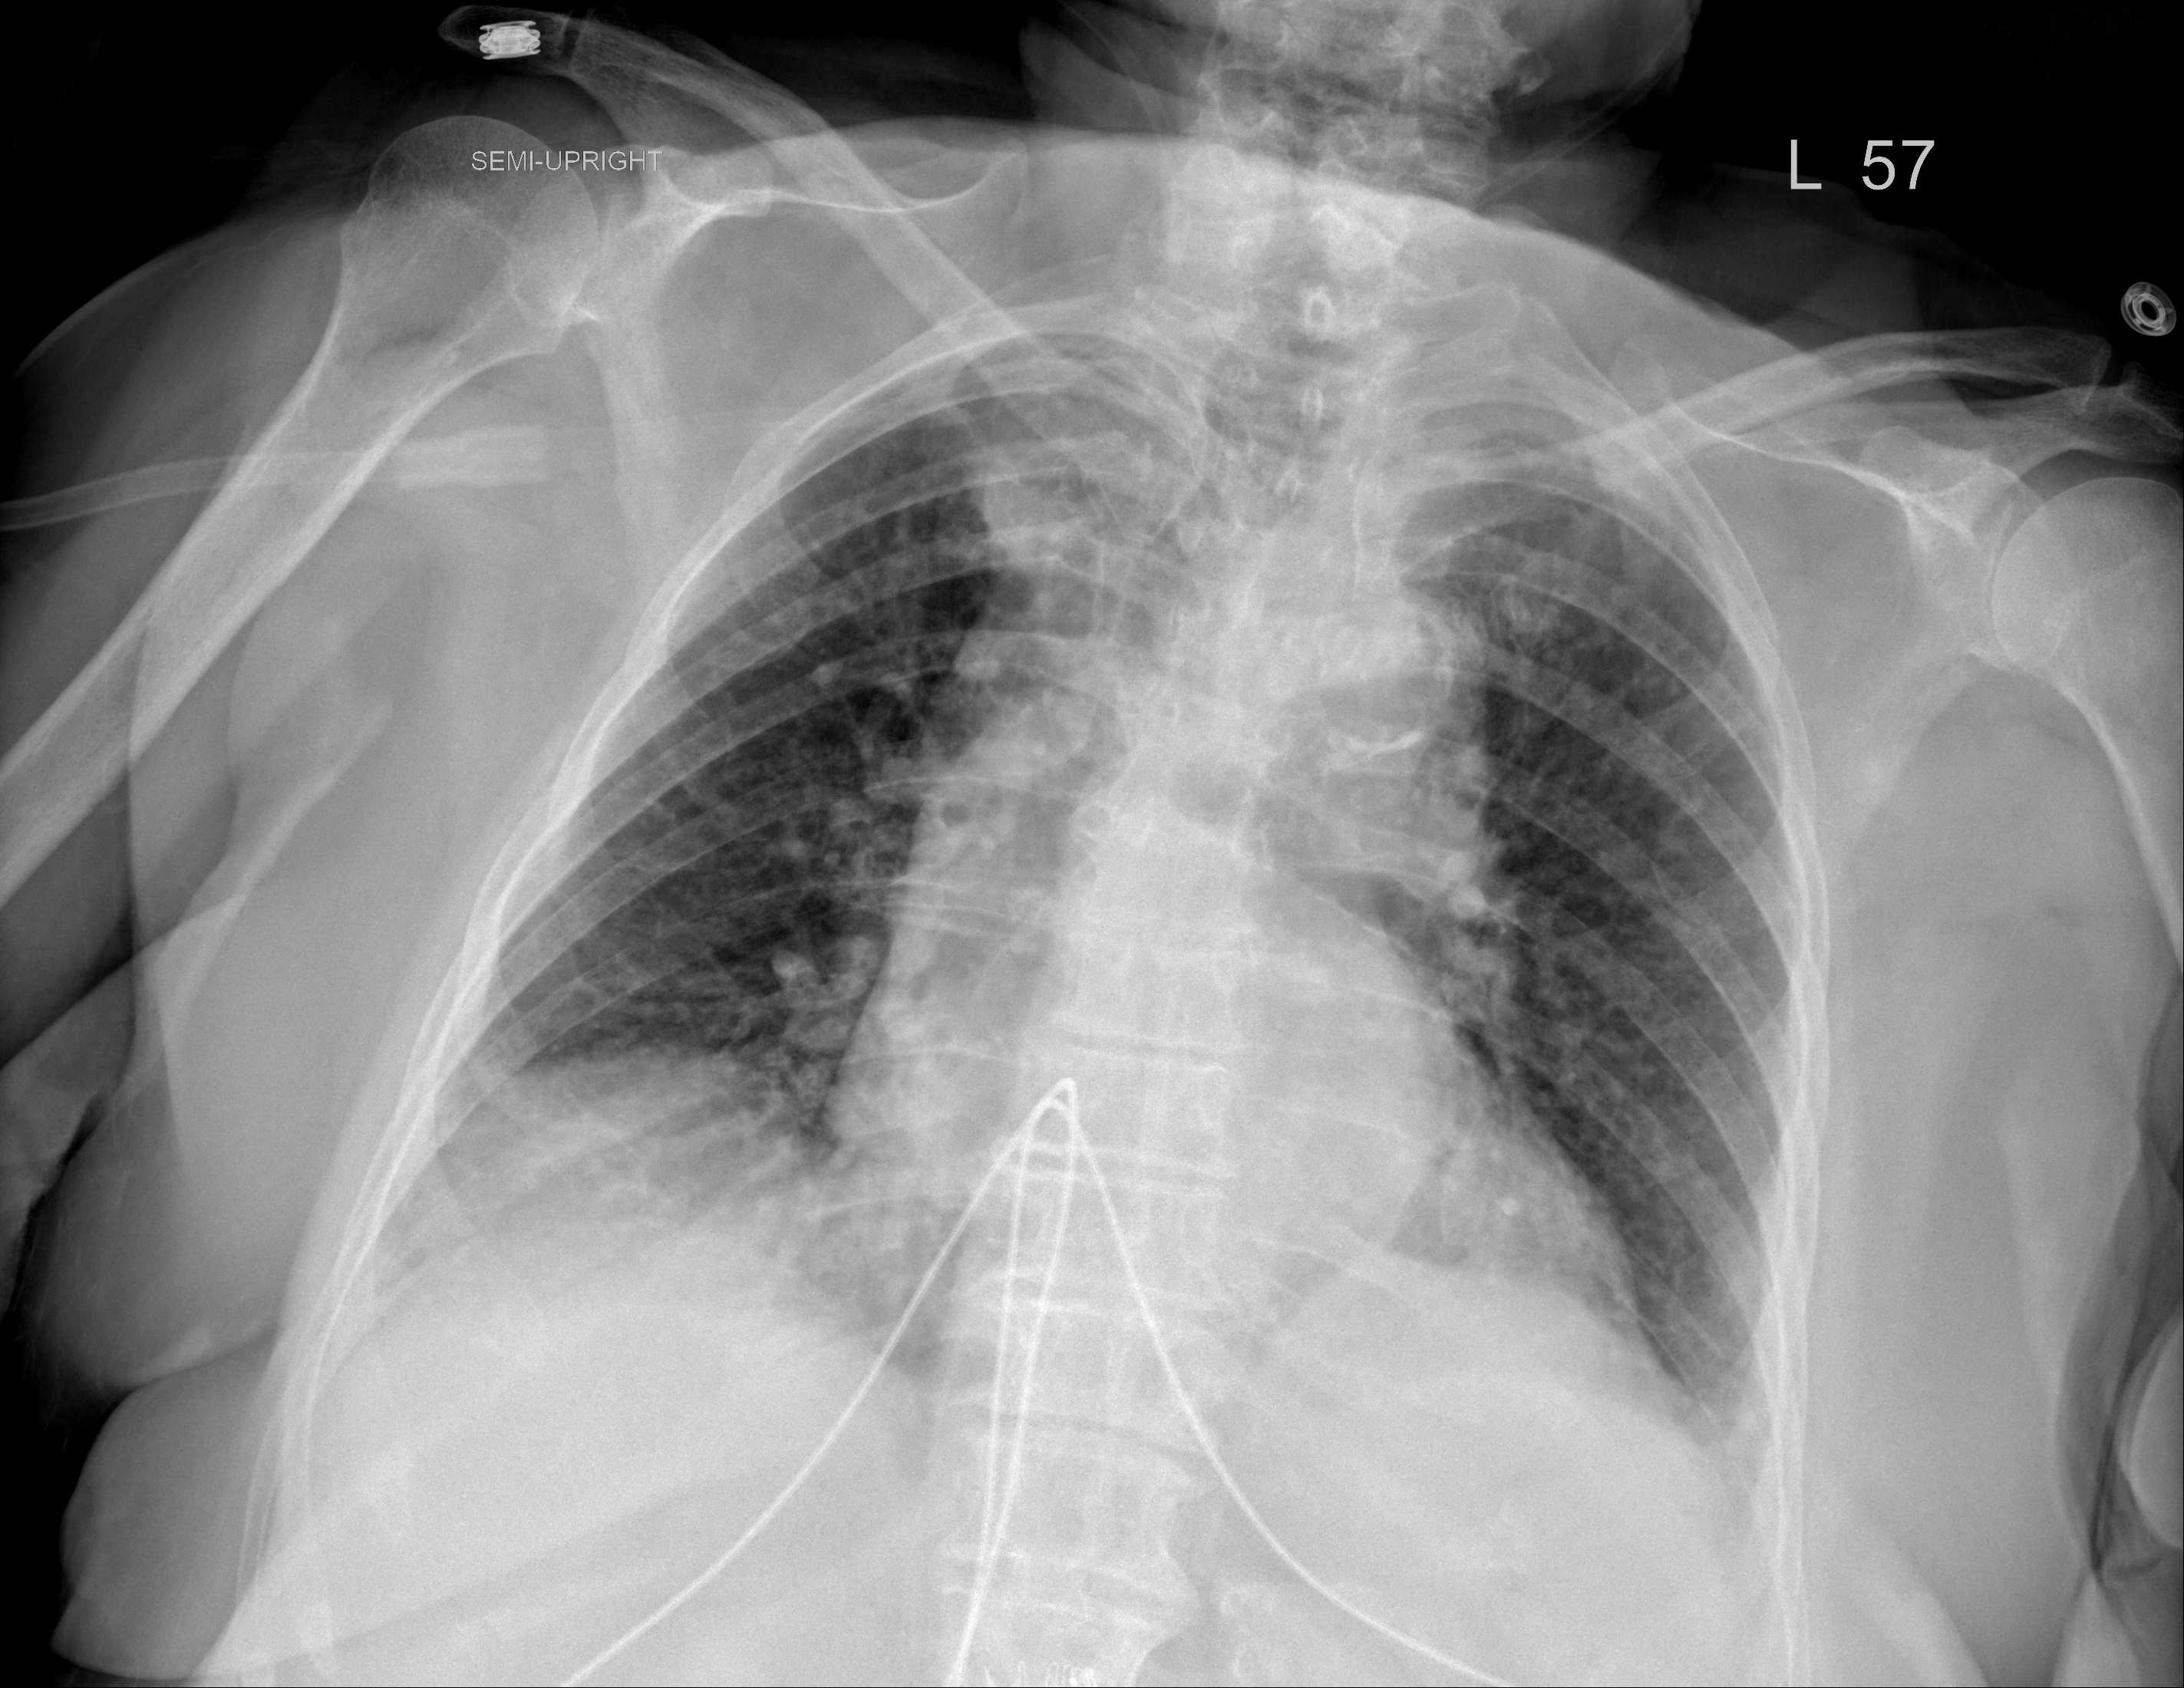
Portable chest radiograph, AP projection. Female patient, age 88 years; COVID-19 (test-positive).
Key findings recorded by the radiologist: Lung volumes remain low but lungs are clear.